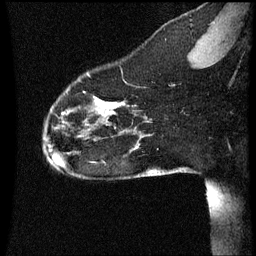
Breast MRI (dynamic contrast-enhanced), one sagittal slice; dynamic contrast-enhanced series, image 2 of 3 at this slice position (ordered by acquisition); 1.5 T; TE 4.2 ms, TR 8.9 ms; 2 mm slice thickness; 256 × 256 image matrix, field of view 200 × 200 mm. Female patient, age 35 years. From the clinical record (not read from this slice): setting: breast cancer imaged before/during neoadjuvant chemotherapy; receptor status: HER2-positive.
Outlined on this slice (semi-automatic segmentation, software-assisted and operator-edited):
- analysis volume of interest (the breast-tissue region the enhancement analysis was run in; not a lesion): box from (x=42, y=66) to (x=177, y=177) px
- tumour enhancement mask (voxels above the 70 % enhancement threshold inside the analysis volume of interest): (x=98, y=100)–(x=121, y=111)